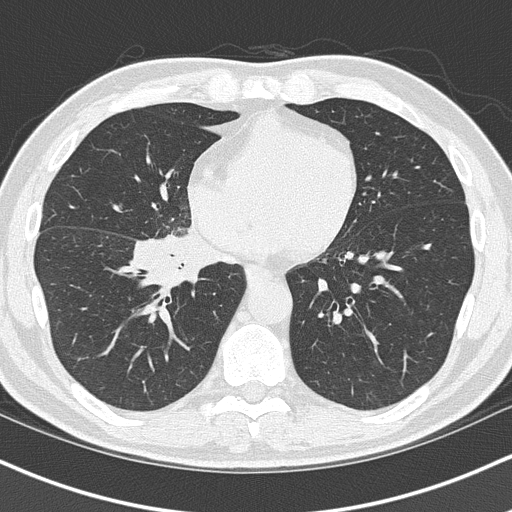
Low-dose screening chest CT, one axial slice. Position 51 of 151 along the scan axis. Reconstruction kernel B50f. Lung window (W 1500 / L -600 HU). 2 mm slice thickness. 512 × 512 image matrix, field of view 320 × 320 mm.
Outlined on this slice (manually delineated by an expert):
- lesion 1 (tumor, hilum of right lung): box from (x=135, y=234) to (x=201, y=285) px